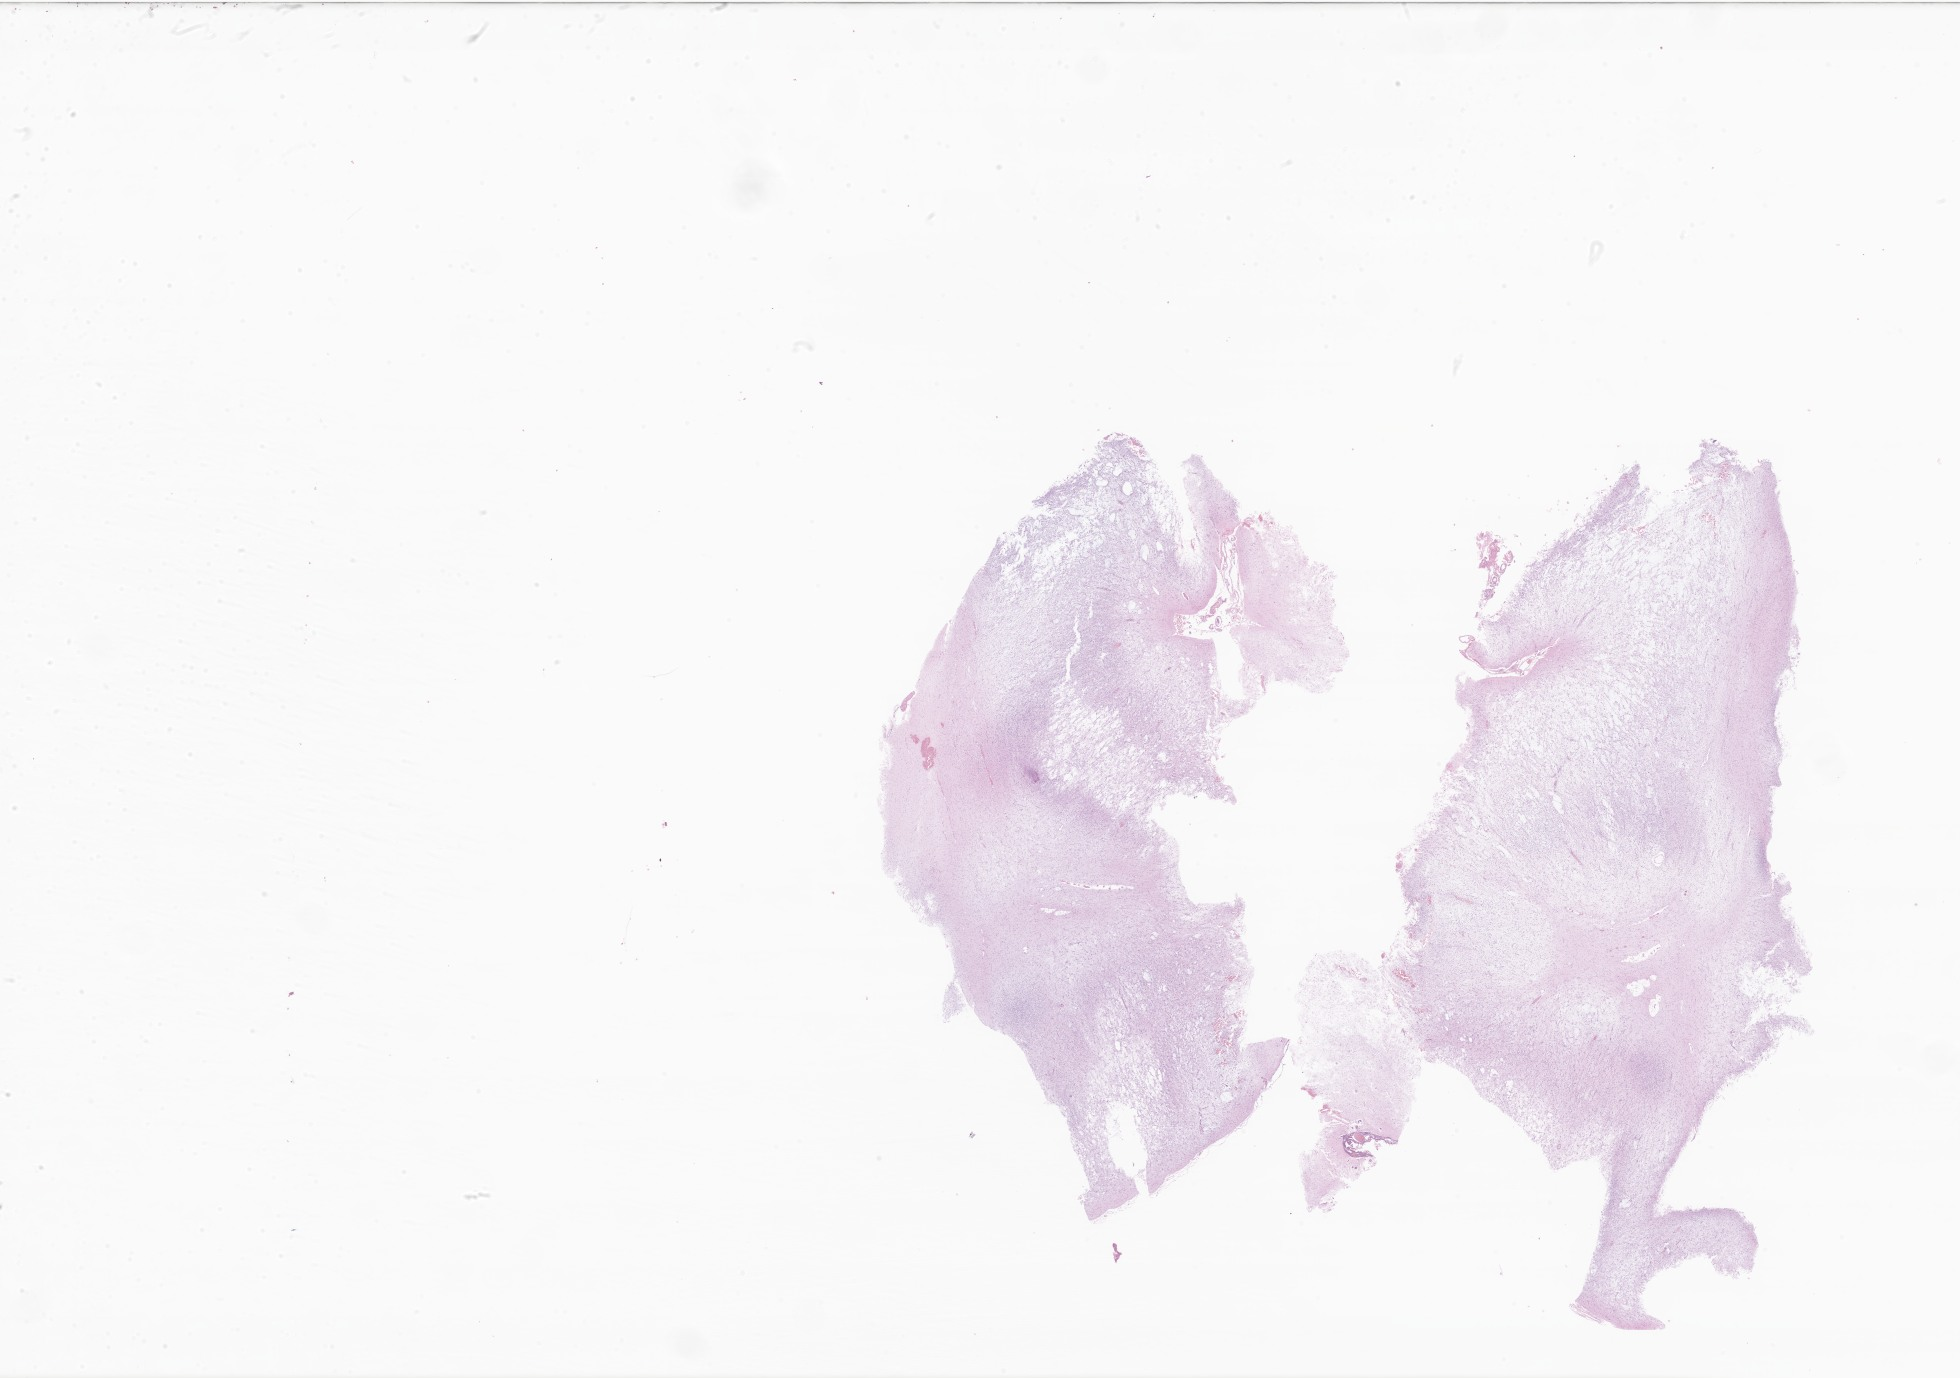
Hematoxylin and eosin (H&E) whole-slide image of tumor tissue from the brain, a low-resolution overview of the entire scanned area, about 33.1 x 23.2 mm. Formalin-fixed paraffin-embedded section. Patient: female, age 150 months (12 years 6 months).
Diagnosis (ICD-O-3 morphology term): Dysembryoplastic neuroepithelial tumor.